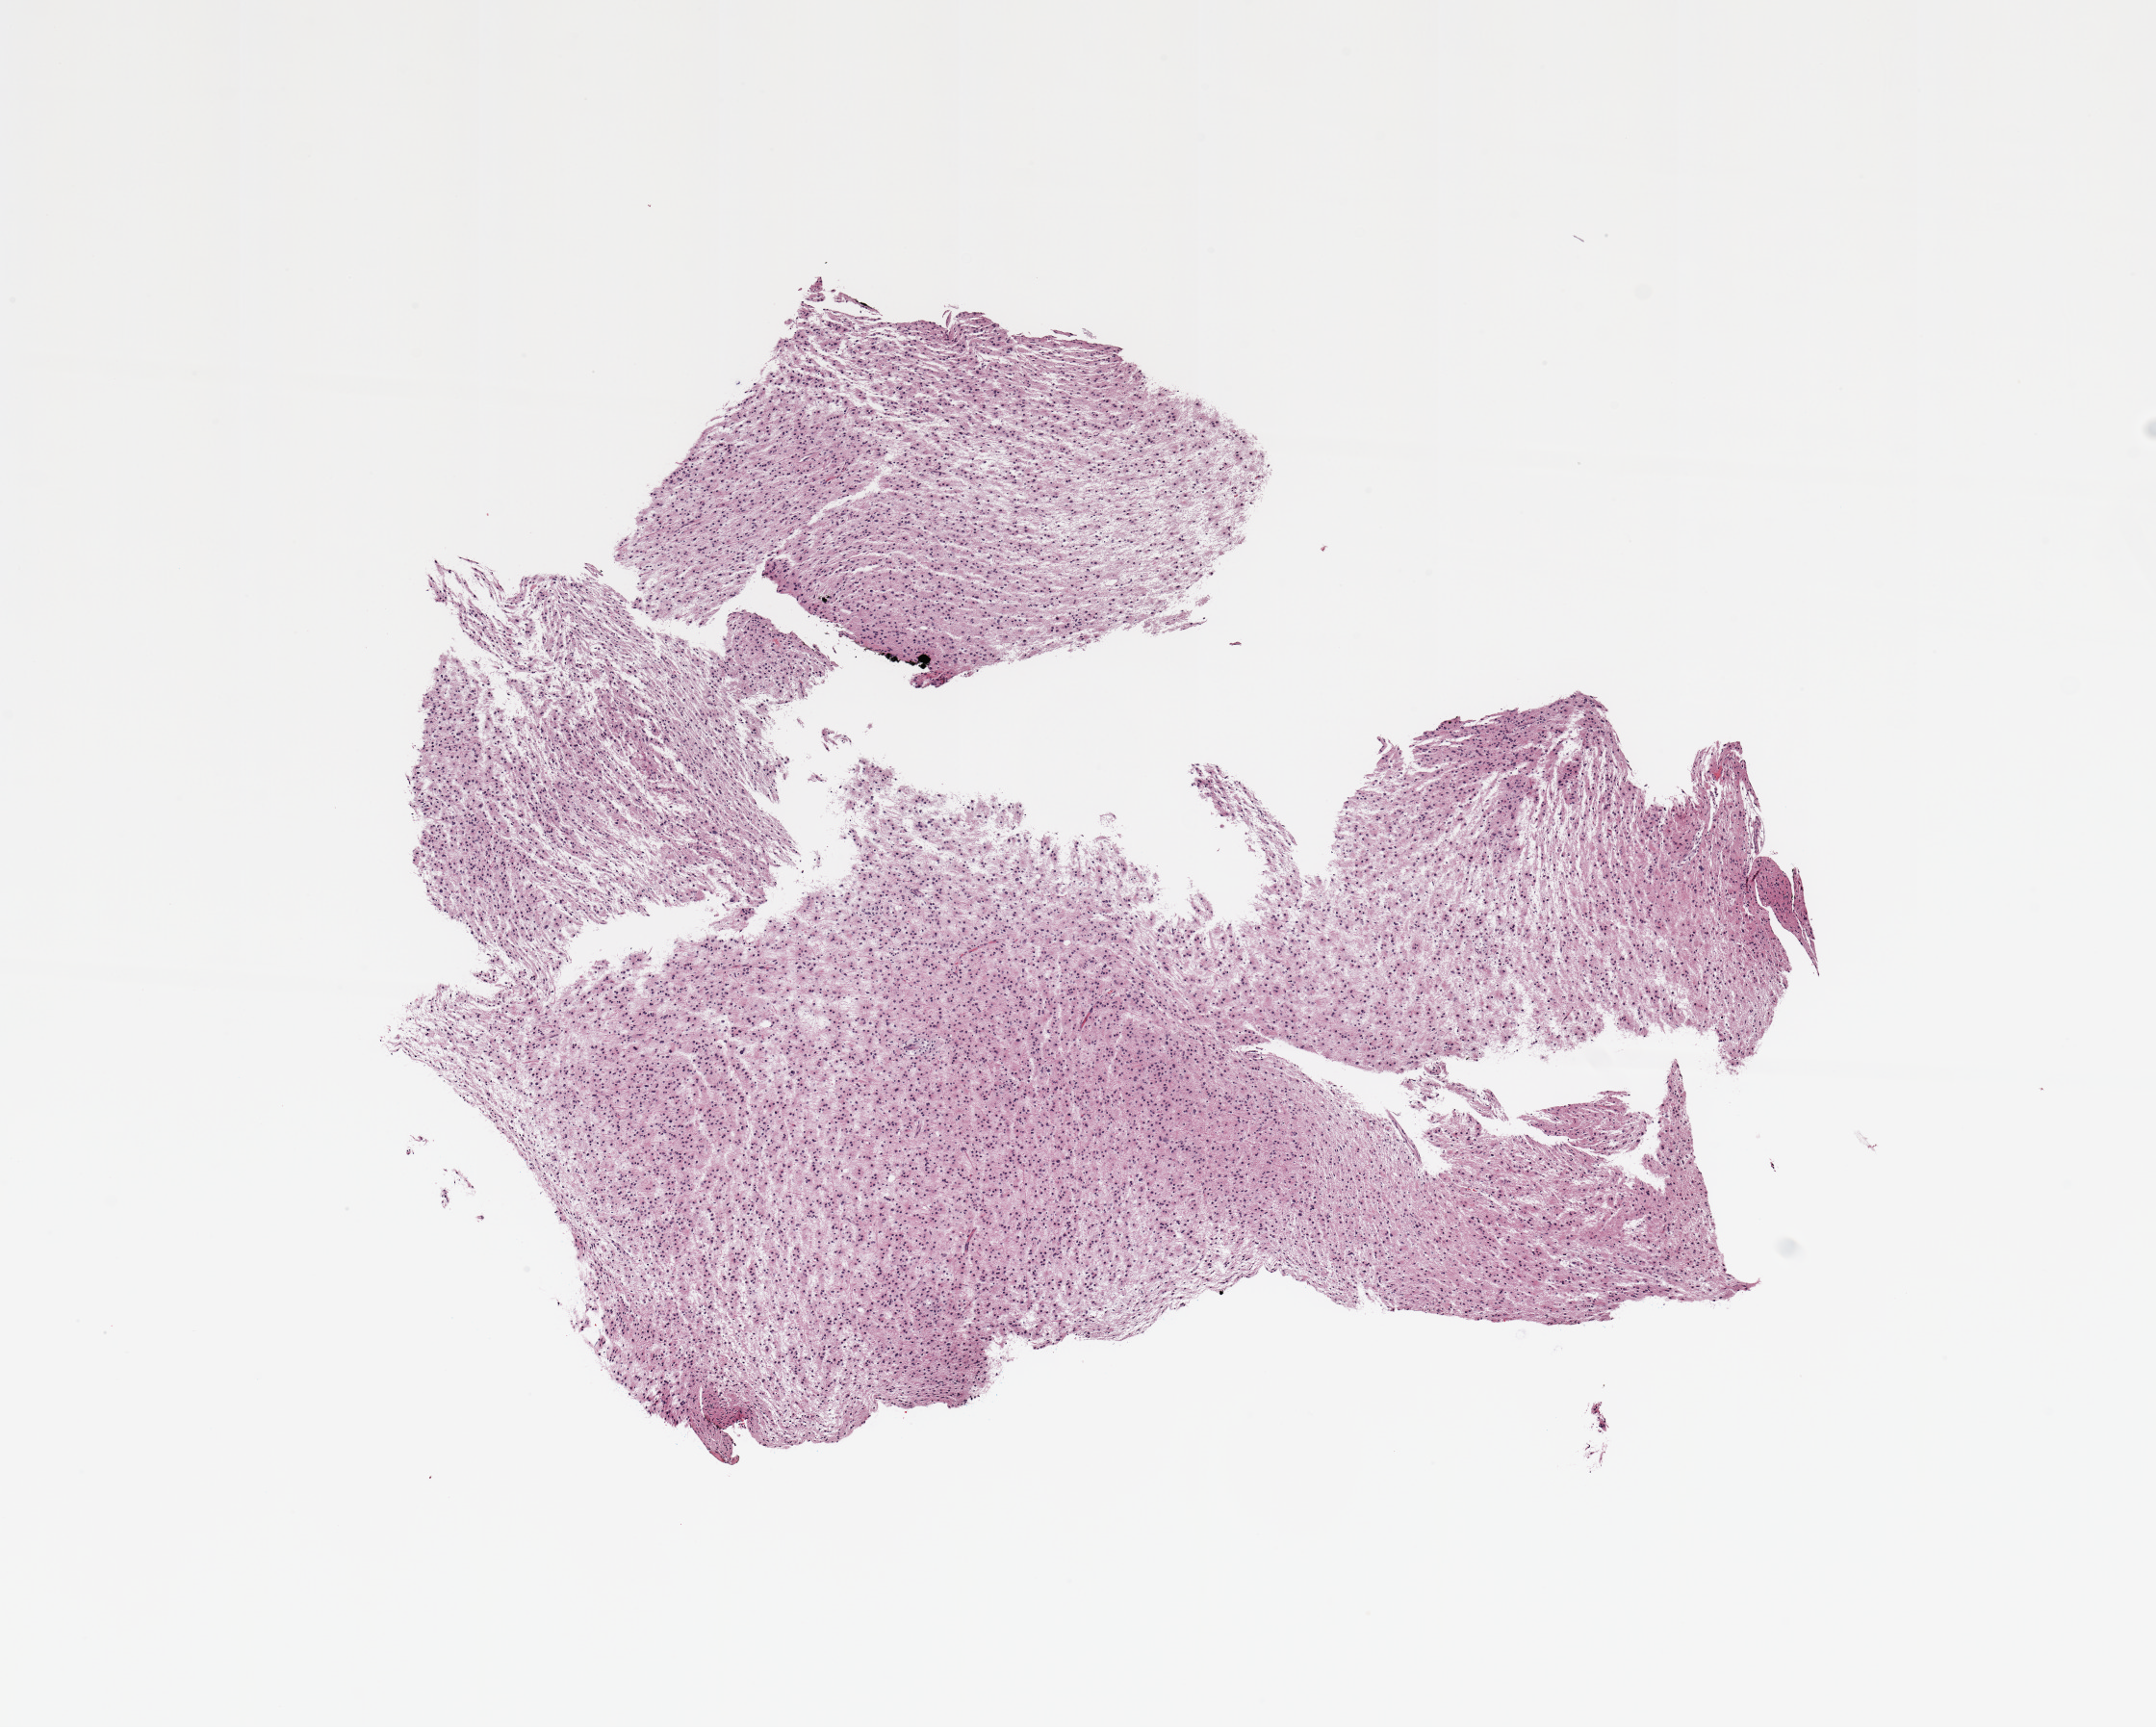
Digitized H&E-stained tissue section (whole slide), whole scanned area (about 8.9 x 7.1 mm, slide scanned at 20x) shown as a low-resolution overview, tumour tissue sample, sampled site: frontal lobe. 34-year-old male patient. Slide review estimates, as recorded: tumour nuclei 75%, necrosis 5%.
Primary tumour site (as recorded): frontal lobe. Diagnosis: Glioblastoma.